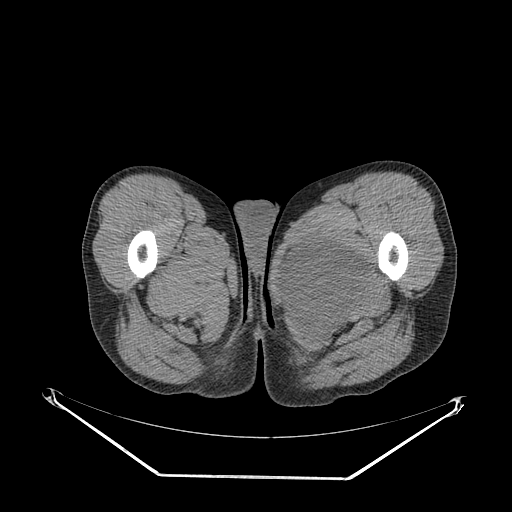
CT of an extremity soft-tissue mass (from a PET/CT study), one axial slice. Position 36 of 267 along the scan axis. 140 kVp. Soft-tissue window (W 400 / L 40 HU). 3.75 mm slice thickness. 512 × 512 image matrix. Male patient. Case-level facts recorded for this patient, not image findings: histological type: pleiomorphic liposarcoma; grade: high; site of the primary tumour: left thigh.
Outlined on this slice (expert contour drawn on MRI and transferred to this co-registered scan by the dataset authors):
- gross tumour volume including surrounding oedema: bounding box [x1, y1, x2, y2] px = [283, 235, 369, 328]
- gross tumour volume (mass): [285, 237, 368, 316]